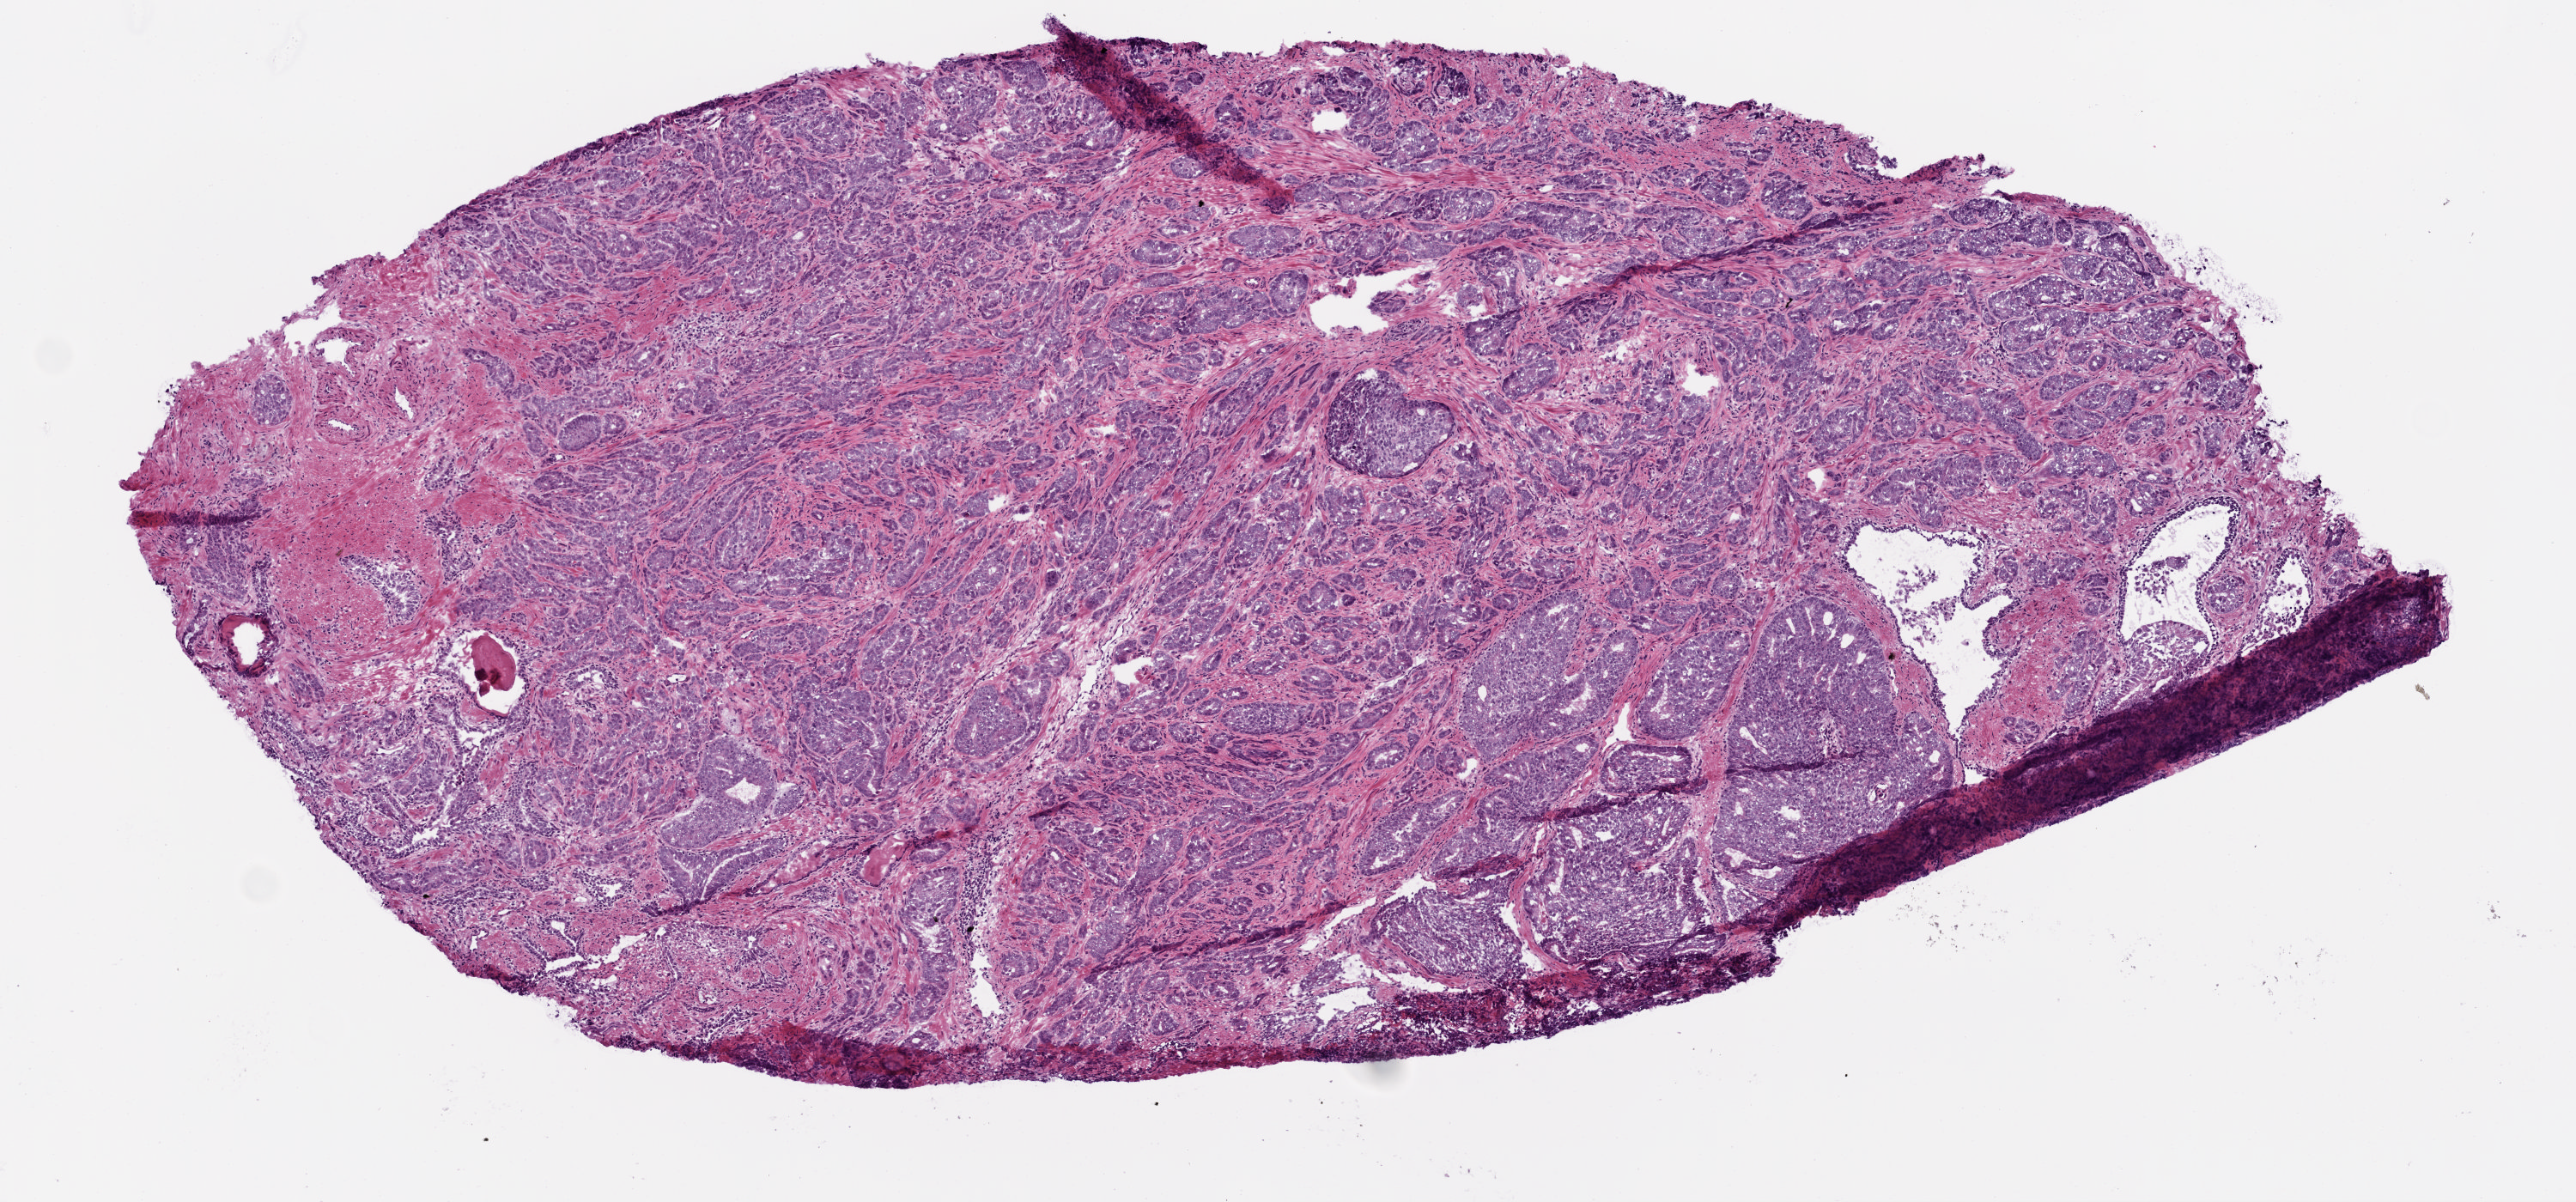
Whole-slide histology image, Hematoxylin and eosin (H&E) stained, a low-resolution overview of the entire scanned area, about 6.0 x 2.8 mm (acquisition: 20x scan), frozen section, primary tumour sample from the prostate. Male, age 65 years at initial diagnosis. Gleason score: 7 (3+4). Pathologist review of this section (percent, as recorded): tumour cells 80%, tumour nuclei 80%, normal cells 10%, stromal cells 10%, necrosis 0%. Infiltration values recorded for this section: lymphocyte infiltration 0%, monocyte infiltration 0%, neutrophil infiltration 0%.
• lymph nodes positive (case pathology): 0 of 4 examined
• laterality: bilateral
• histologic diagnosis: Acinar cell carcinoma